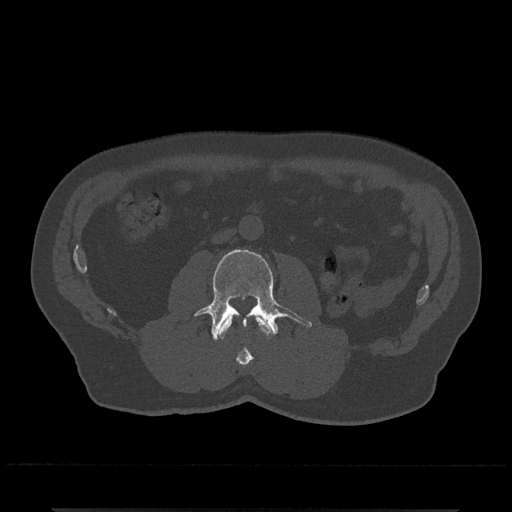
CT including the spine, one axial slice. Slice 237 of 797 in the series (ordered by position). 120 kVp. Bone window (W 1800 / L 400 HU). 512 × 512 image matrix, field of view 393 × 393 mm. Patient: male, 67 years. From the clinical record (not read from this slice): primary cancer: prostate.
Annotated regions visible in this slice (semi-automatically segmented with operator editing):
- L2 vertebra: bounding box [x1, y1, x2, y2] px = [218, 315, 271, 366]
- L3 vertebra: [195, 249, 312, 341]